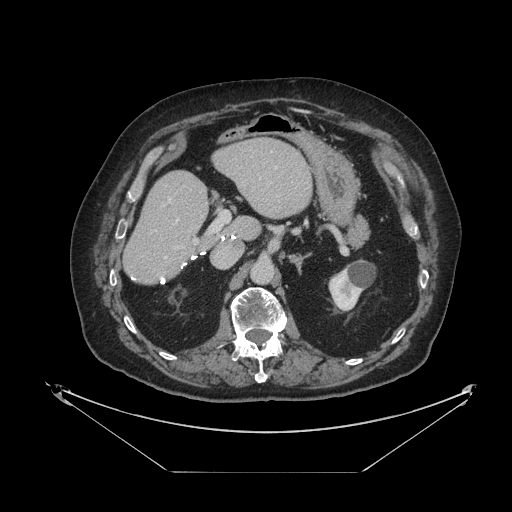
Contrast-enhanced abdominal CT, one axial slice; slice 55 of 121 in the series (ordered by position); soft-tissue window (W 400 / L 40 HU); 2.5 mm slice thickness; 512 × 512 image matrix, field of view 500 × 500 mm. Male patient, age 68 years. From the clinical record (not read from this slice): diagnosis: colorectal cancer liver metastases, imaged before liver resection; multiple liver metastases: no; largest metastasis: 4 cm.
Structures marked on this image (manually delineated by an expert):
- hepatic veins: bounding box (x1, y1, x2, y2) in pixels: (165, 167, 277, 258)
- liver: (124, 139, 312, 283)
- planned liver remnant (the part of the liver to remain after resection): (124, 139, 312, 283)
- portal vein (with intrahepatic branches): (169, 199, 230, 249)